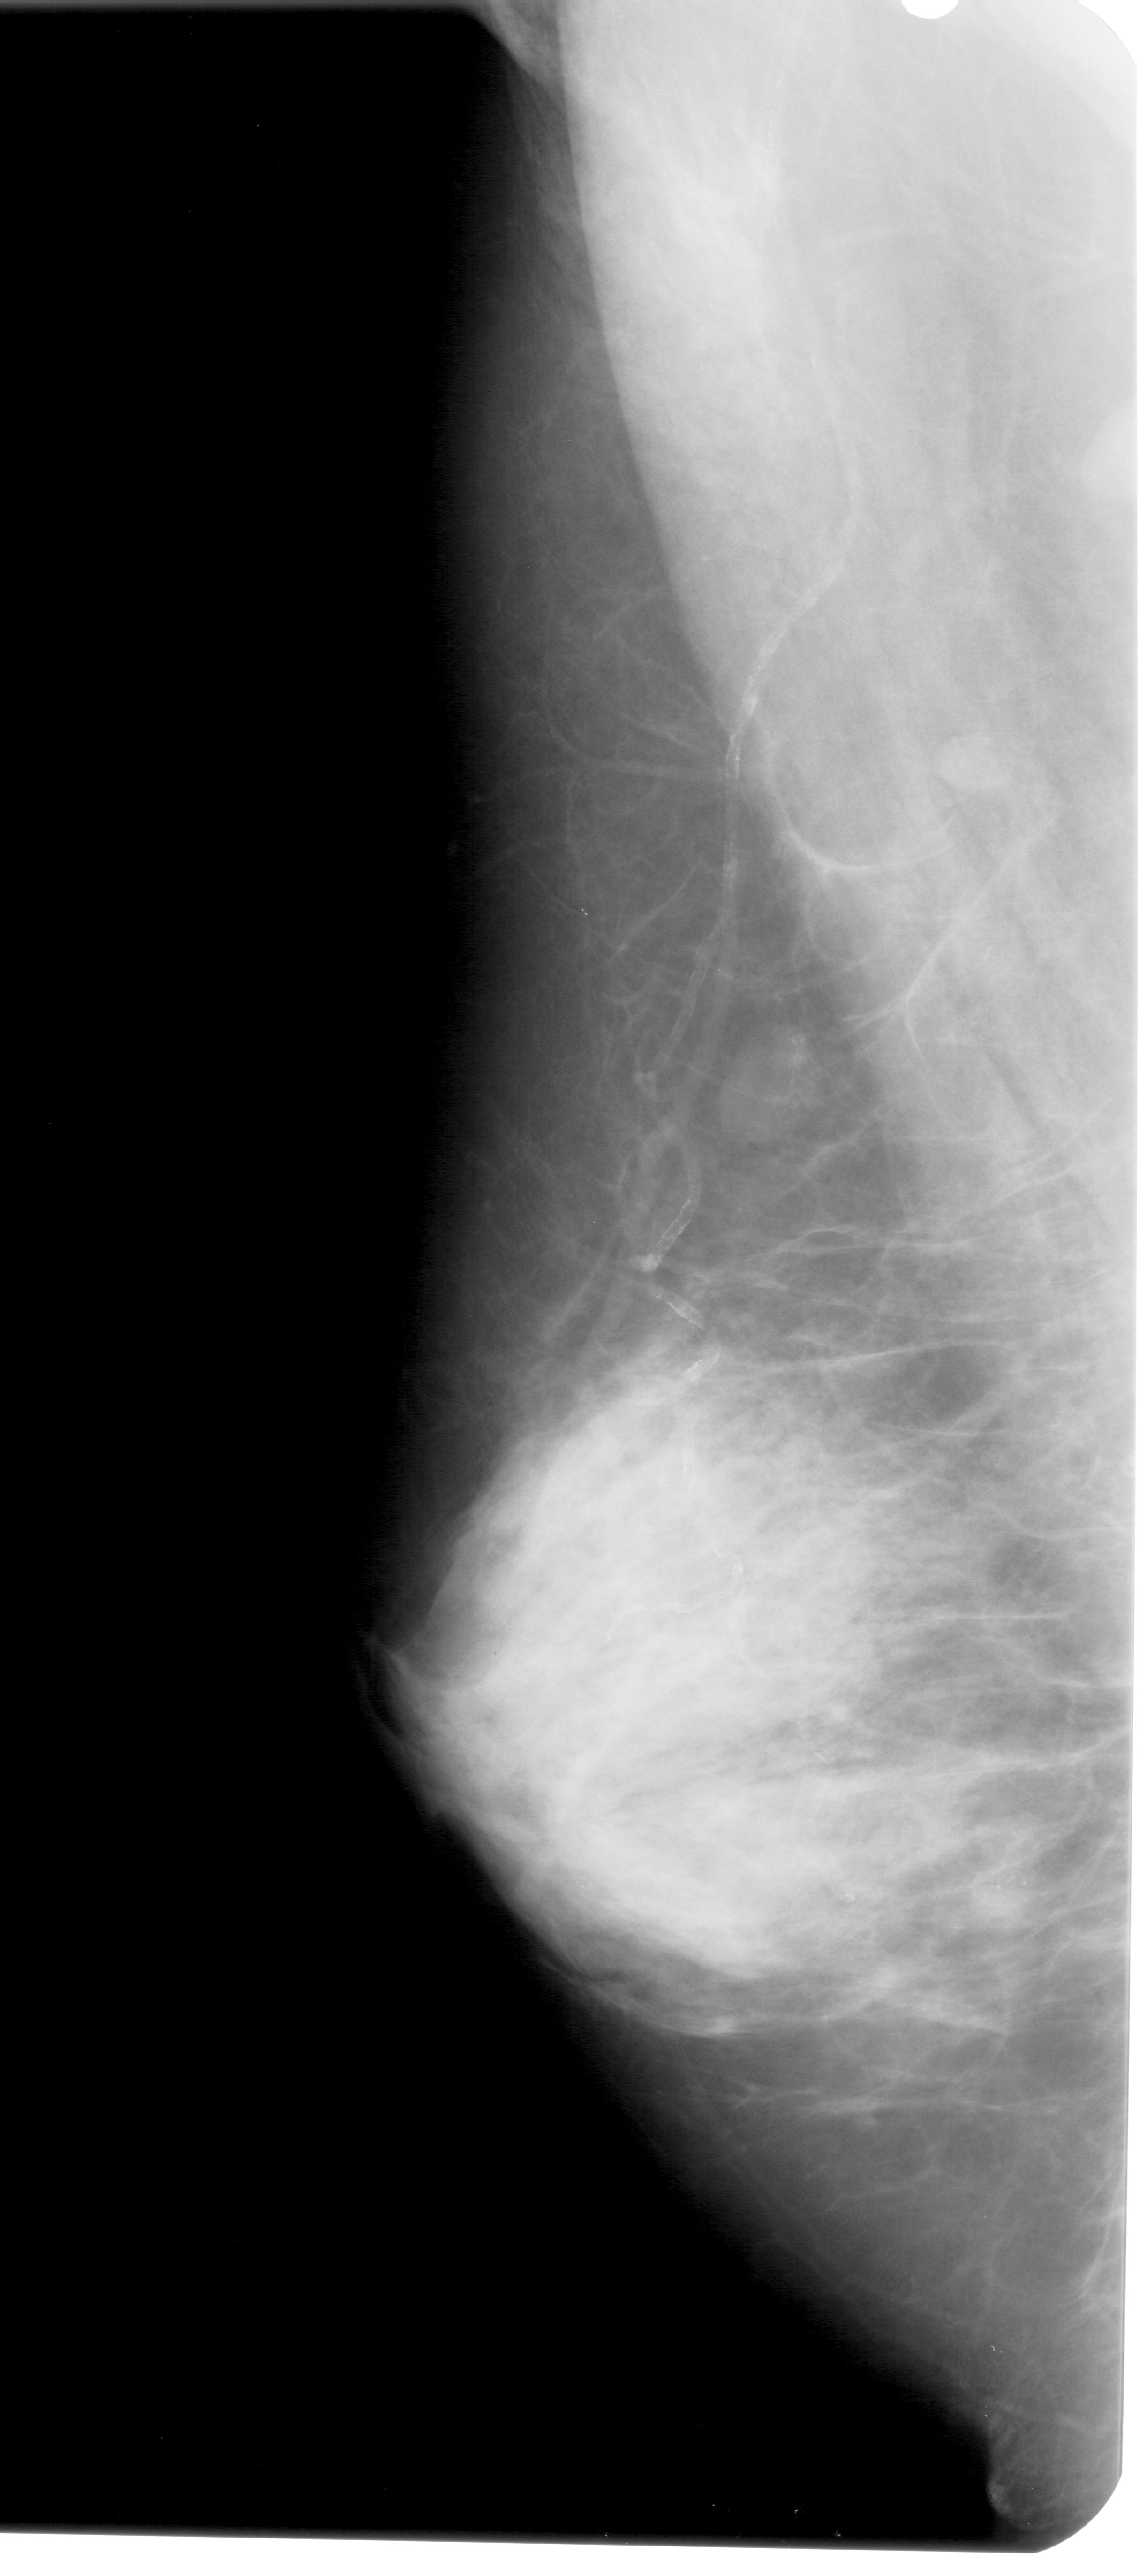
Scanned film-screen mammogram. Left breast. Mediolateral oblique (MLO) view. 1147 × 2576 image matrix.
Expert-marked regions of interest on this film, with their recorded descriptors:
- calcifications, morphology pleomorphic, distribution clustered; BI-RADS assessment category 4; pathology (as recorded): benign: bounding box (x1, y1, x2, y2) in pixels: (941, 1852, 1045, 1922)